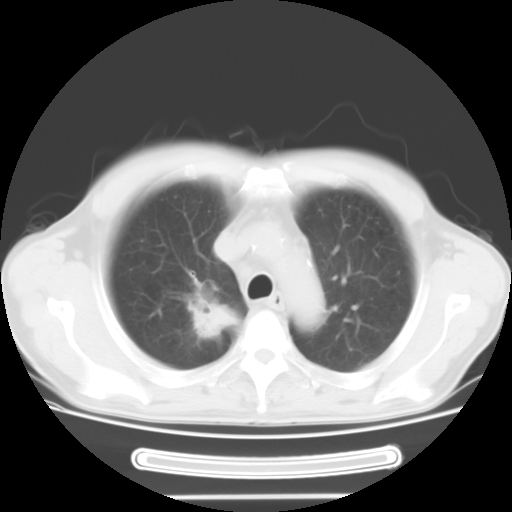
Chest CT, one axial slice. Position 18 of 24 along the scan axis. Reconstruction kernel STANDARD. Lung window (W 1500 / L -600 HU). 512 × 512 image matrix. Patient: male, 57 years. Case-level facts recorded for this patient, not image findings: clinical TNM (as recorded): T2 N3 M1b.
Annotated regions visible in this slice (rectangle marked by the reading radiologist):
- lung tumour (recorded histology: adenocarcinoma): bounding box [x1, y1, x2, y2] px = [191, 300, 241, 338]